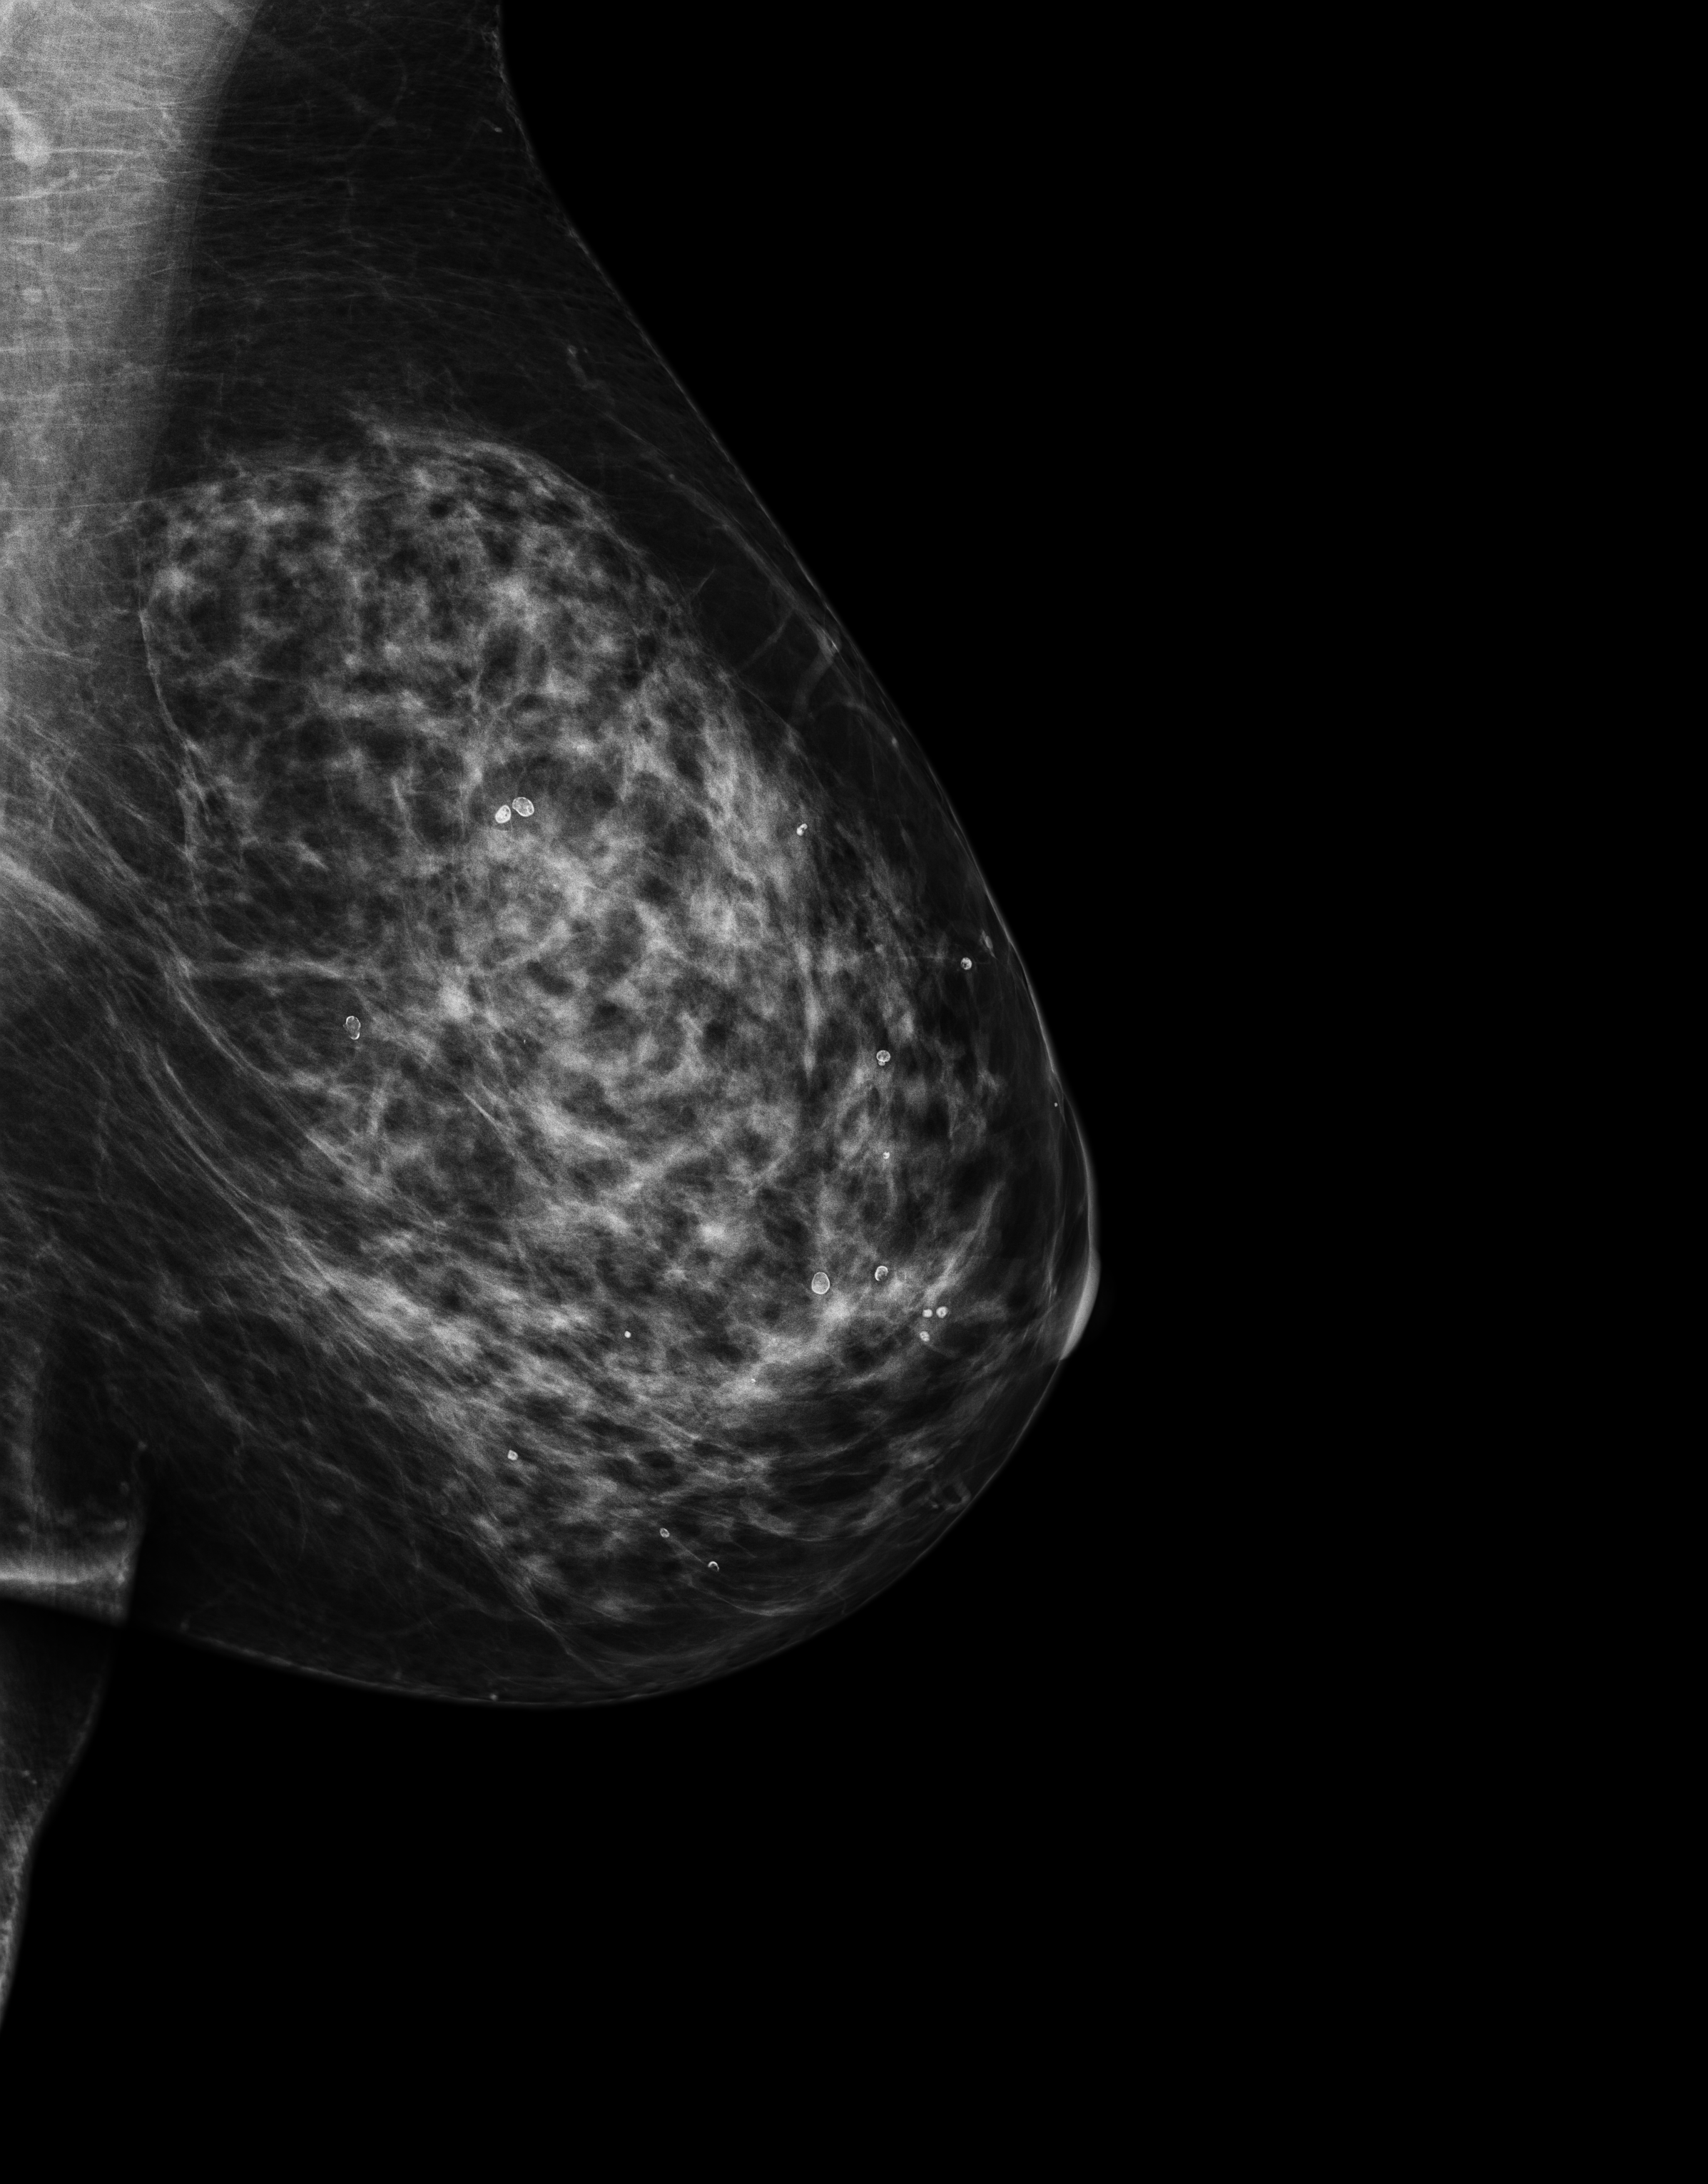
Digital mammogram (FFDM), left breast, medio-lateral oblique projection, screening examination, compressed breast thickness 70 mm, system: Senographe Essential ADS_56.21.3. Female patient, age 66 years.
- BI-RADS breast density category at the screening exam (both breasts, scale 1–4): 3
- final BI-RADS category for the screening round (tomosynthesis exam, both breasts): category 1
- recall: no recall after this screen